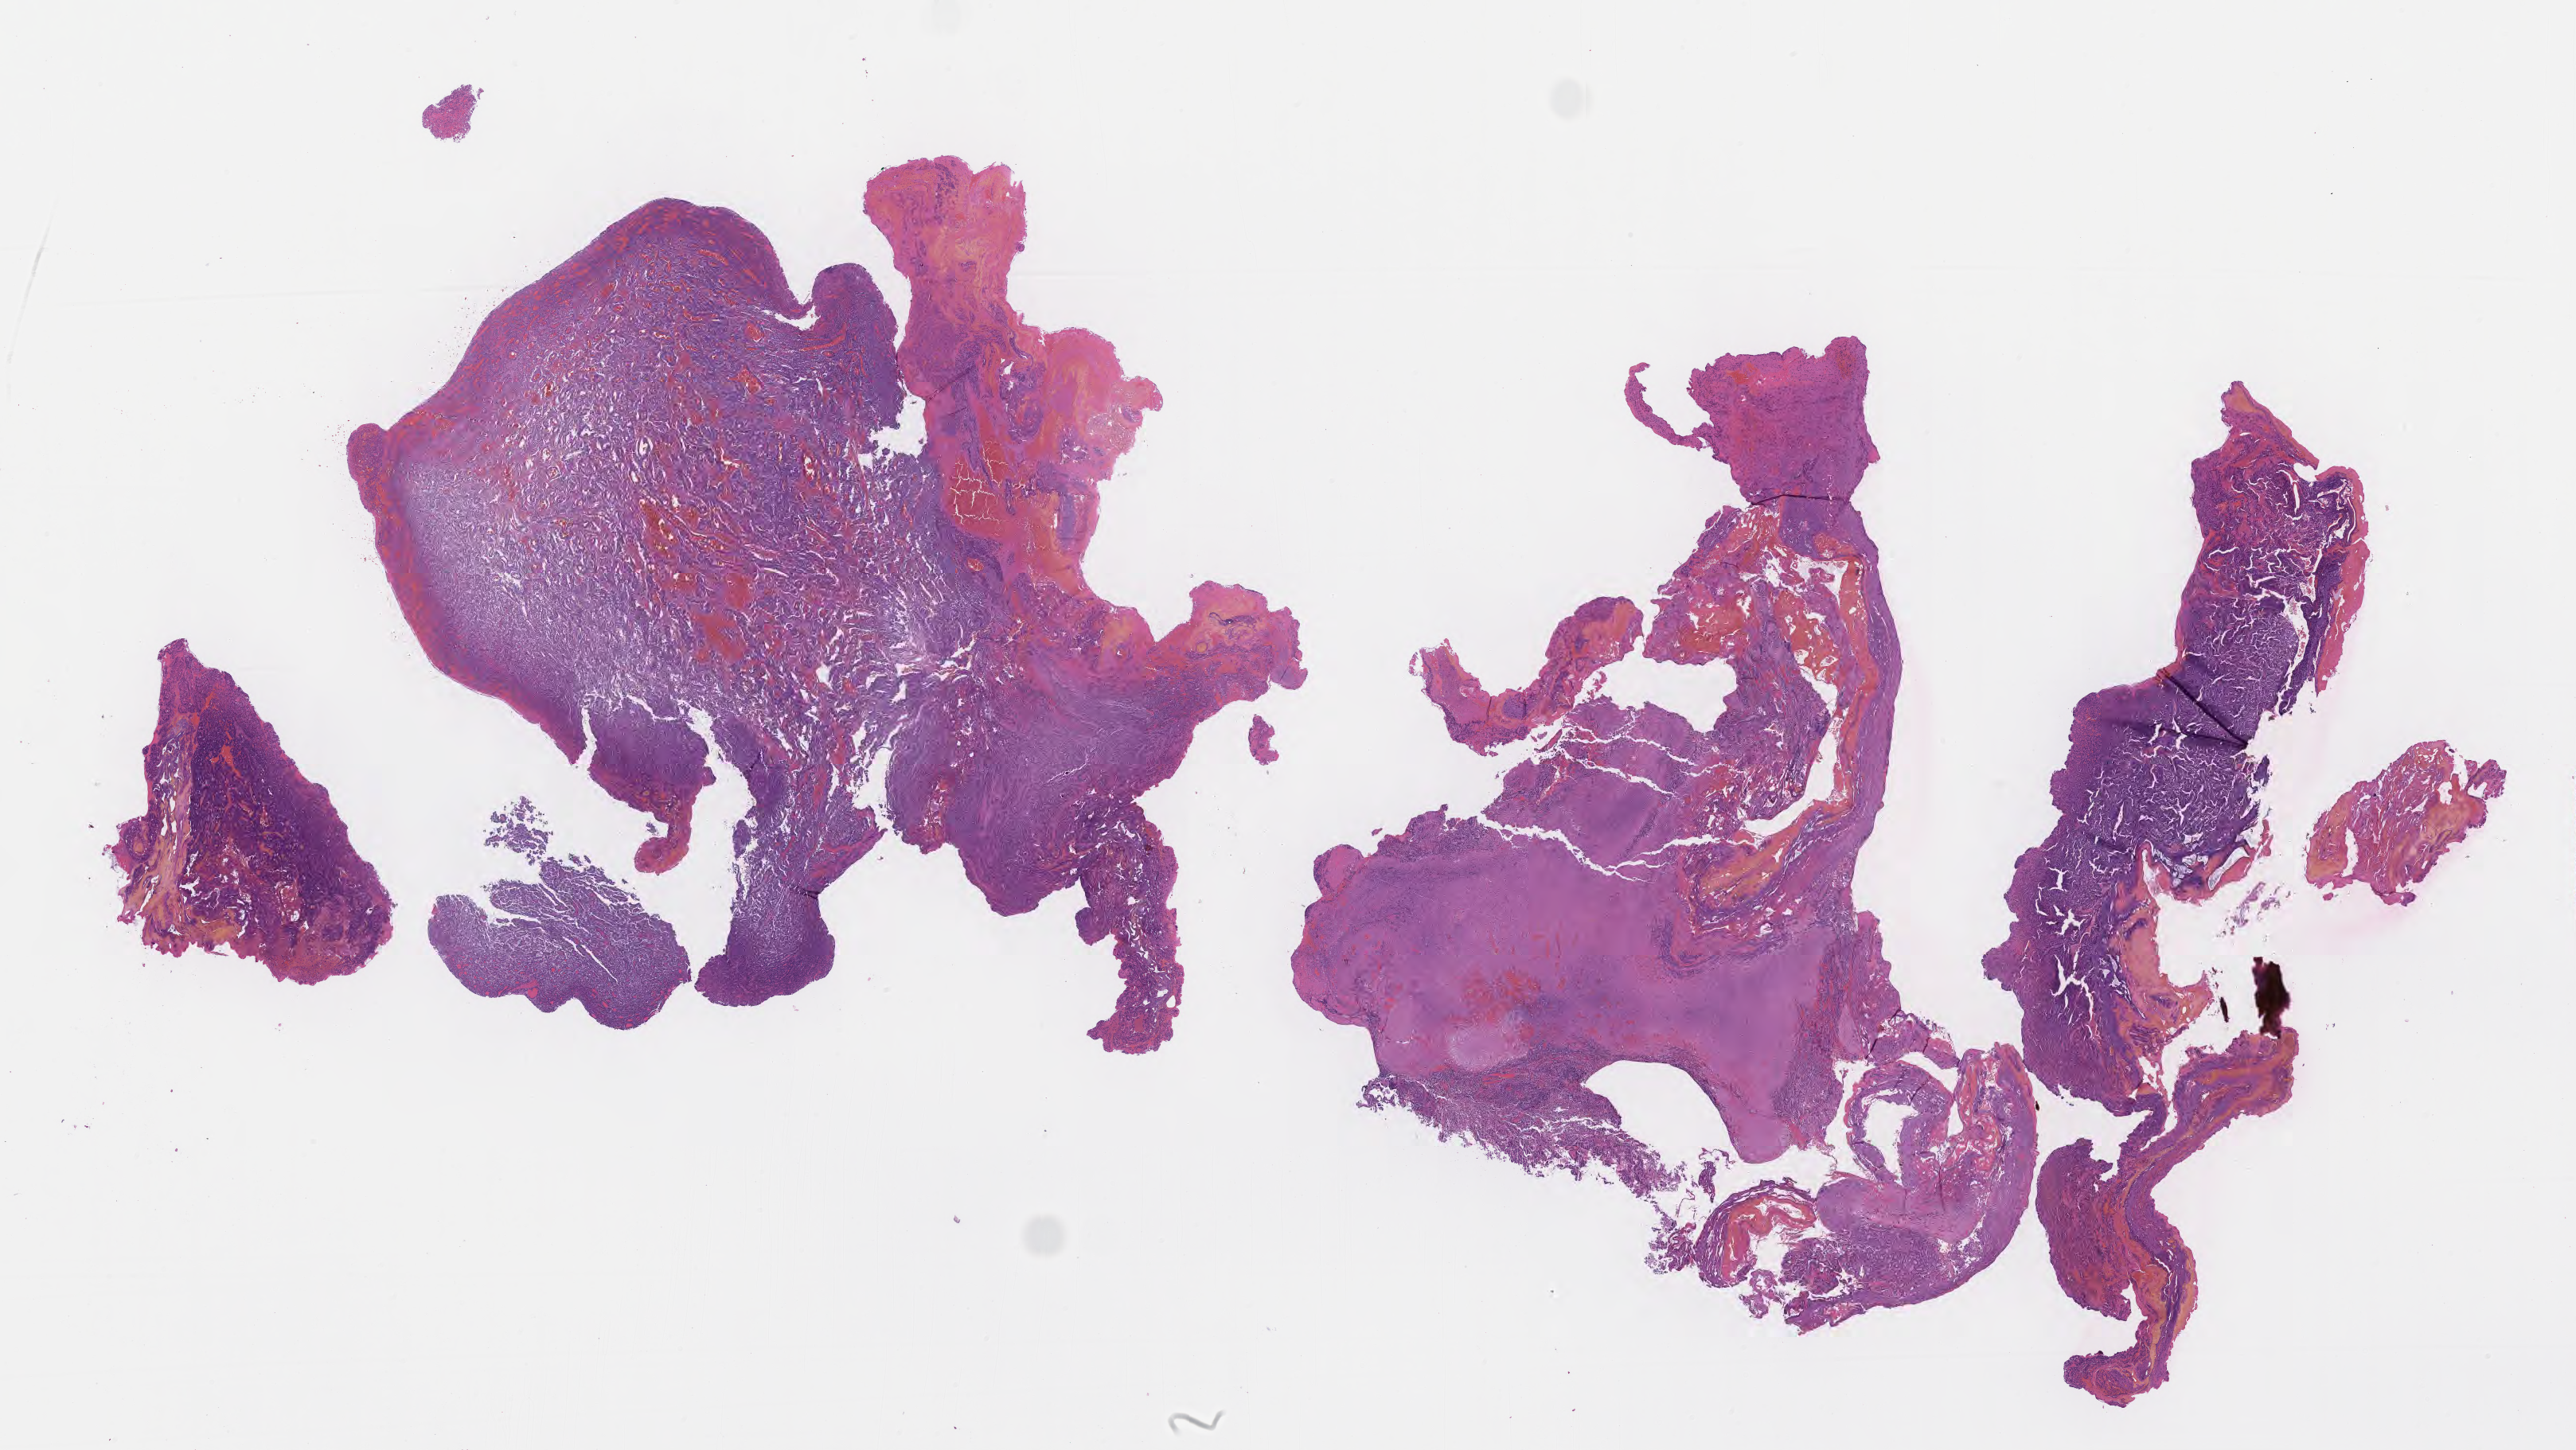
Haematoxylin and eosin whole-slide image of tumor tissue from the brain — a low-resolution overview of the entire scanned area, about 26.2 x 14.7 mm, formalin-fixed paraffin-embedded section. Patient male; age 73 months (6 years 1 month).
* diagnosis (ICD-O-3 morphology term): Neoplasm, uncertain whether benign or malignant